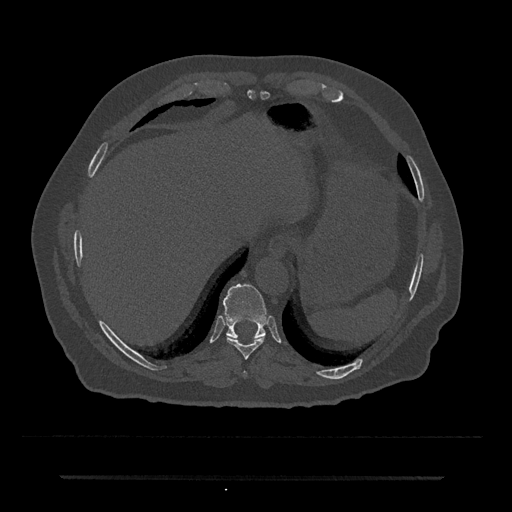
CT including the spine, one axial slice. Slice 258 of 797 in the series (ordered by position). 120 kVp. Bone window (W 1800 / L 400 HU). 0.5 mm slice thickness. 512 × 512 image matrix, field of view 437 × 437 mm. Patient: male, 69 years. From the clinical record (not read from this slice): primary cancer: prostate.
Annotated regions visible in this slice (semi-automatically segmented with operator editing):
- T10 vertebra: box from (x=223, y=284) to (x=267, y=338) px
- T8 vertebra: (x=244, y=372)–(x=246, y=375)
- T9 vertebra: (x=226, y=336)–(x=265, y=359)